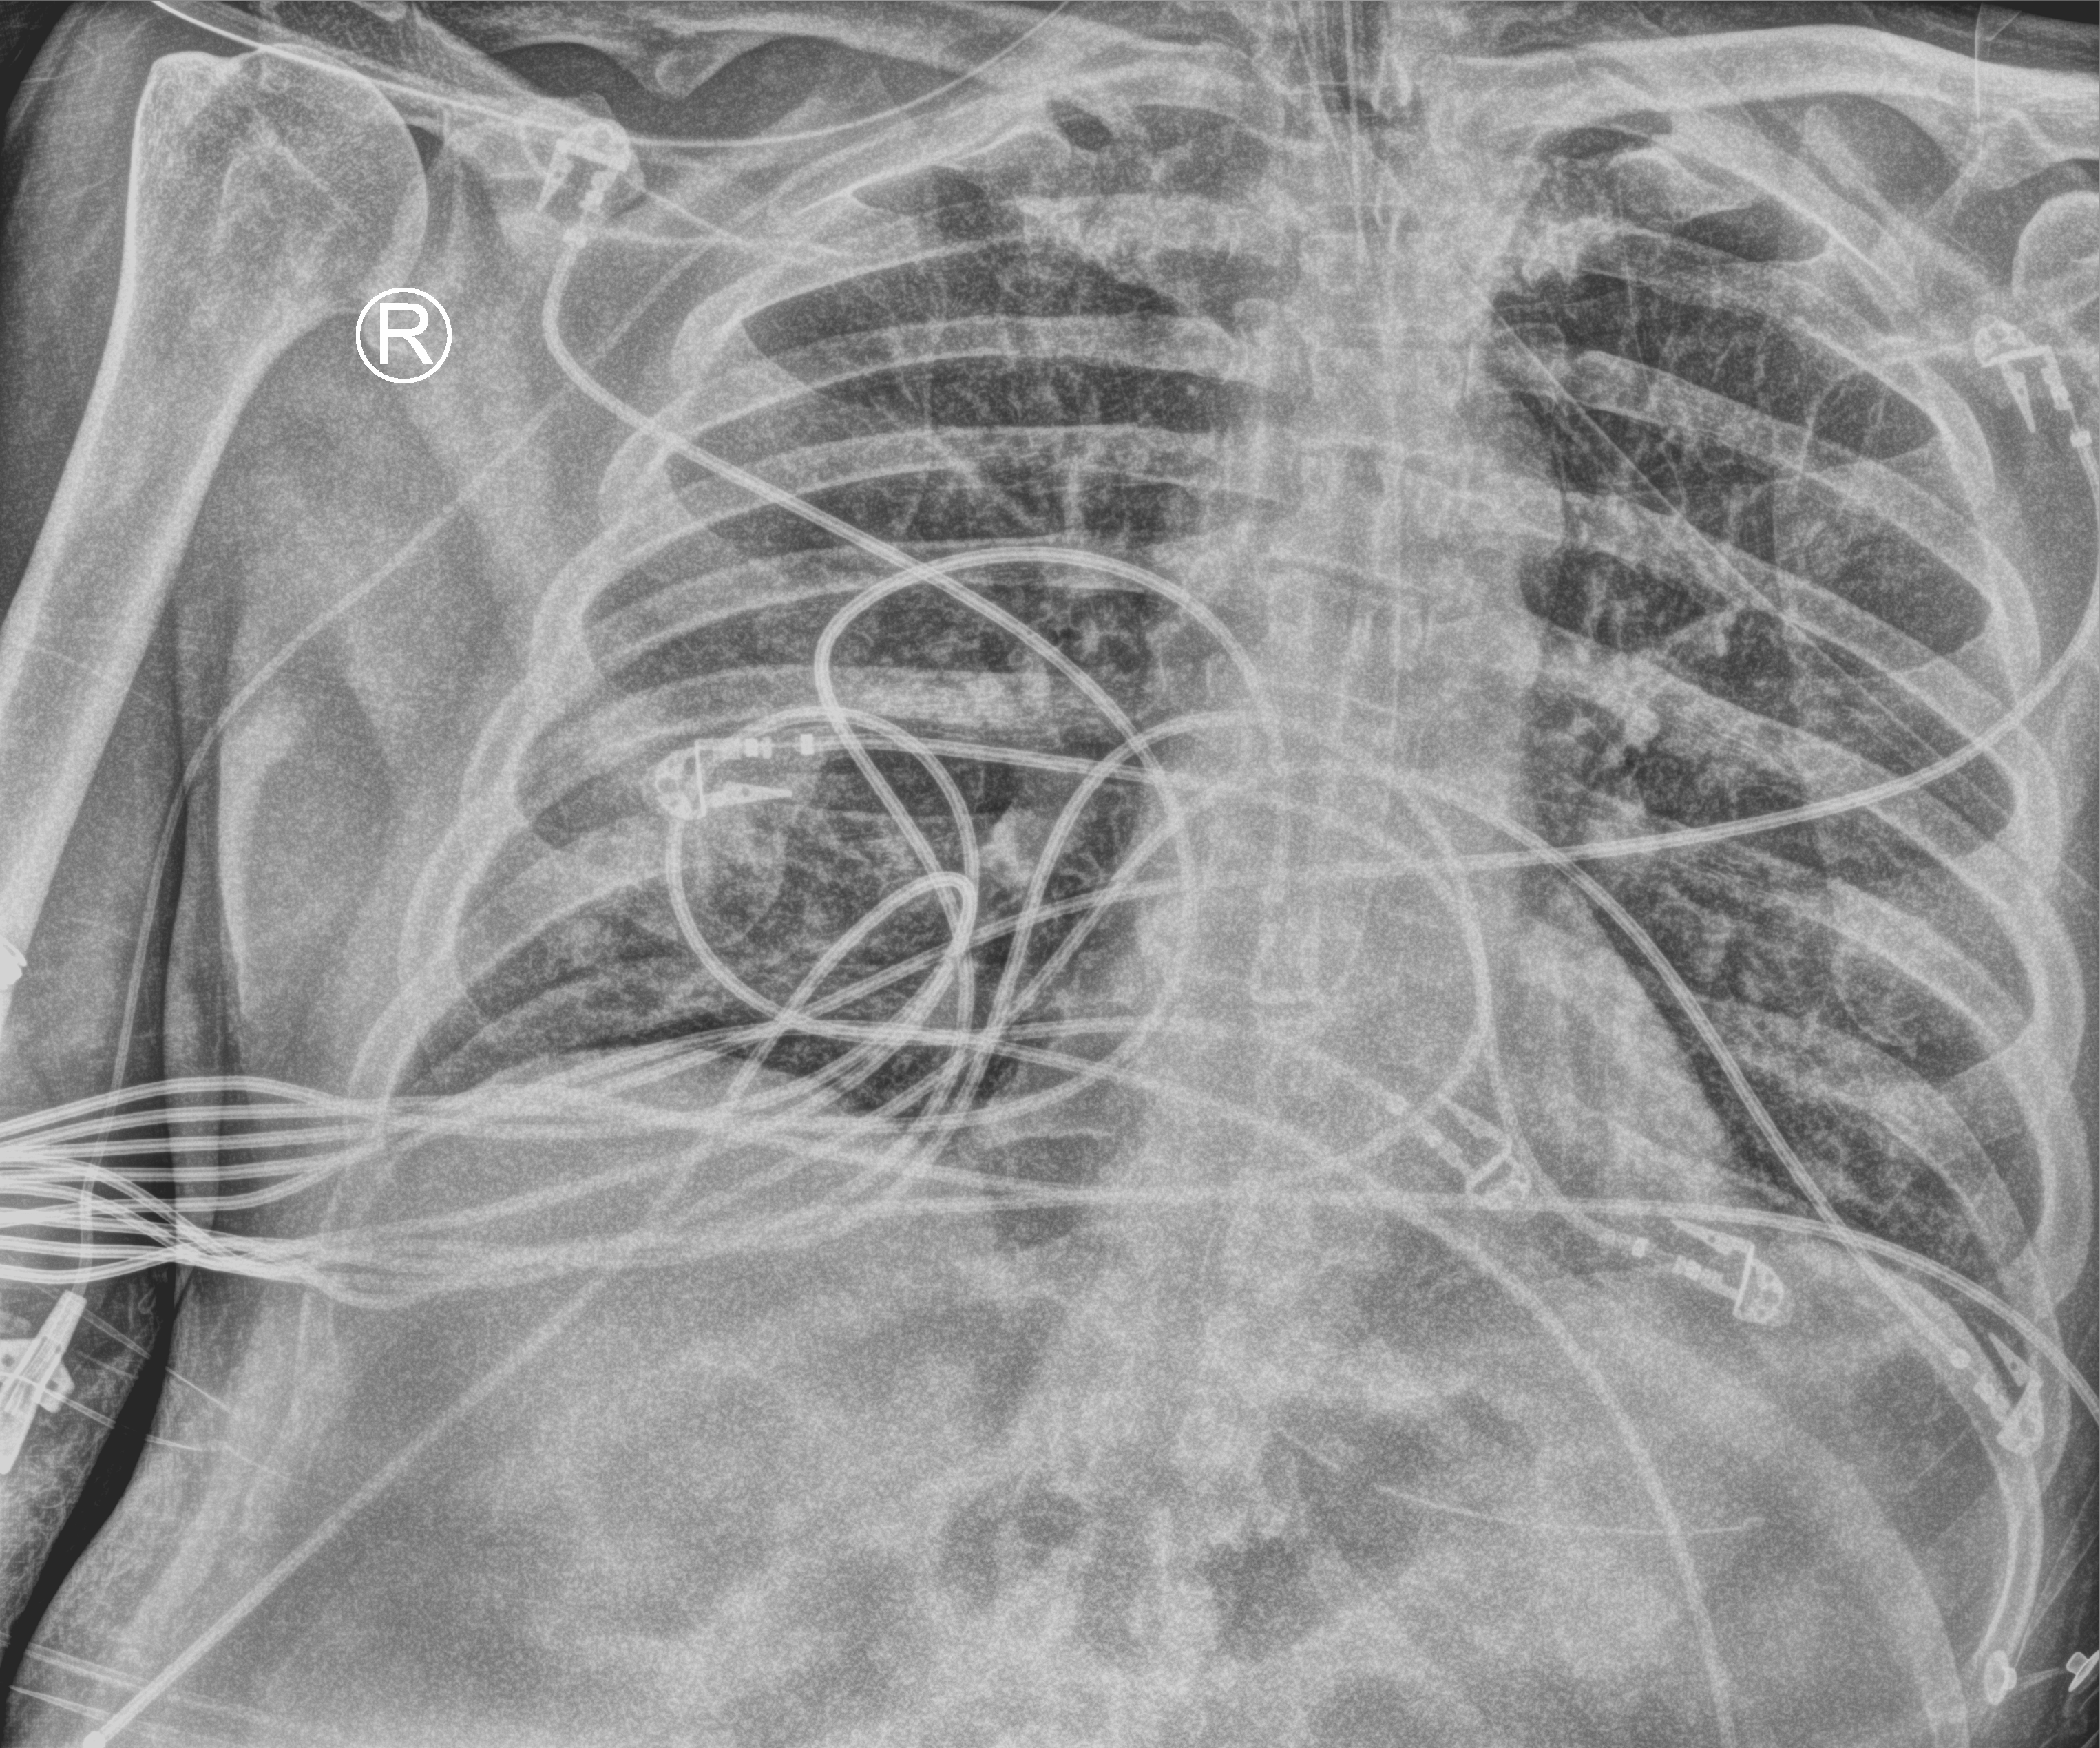
Chest X-ray (portable), anteroposterior (AP) projection. Patient hospitalised with COVID-19; male, aged 60–74 years.
Hospital-stay facts (about this admission, not read from this image; timing relative to this image not recorded):
- length of hospital stay: 26 days